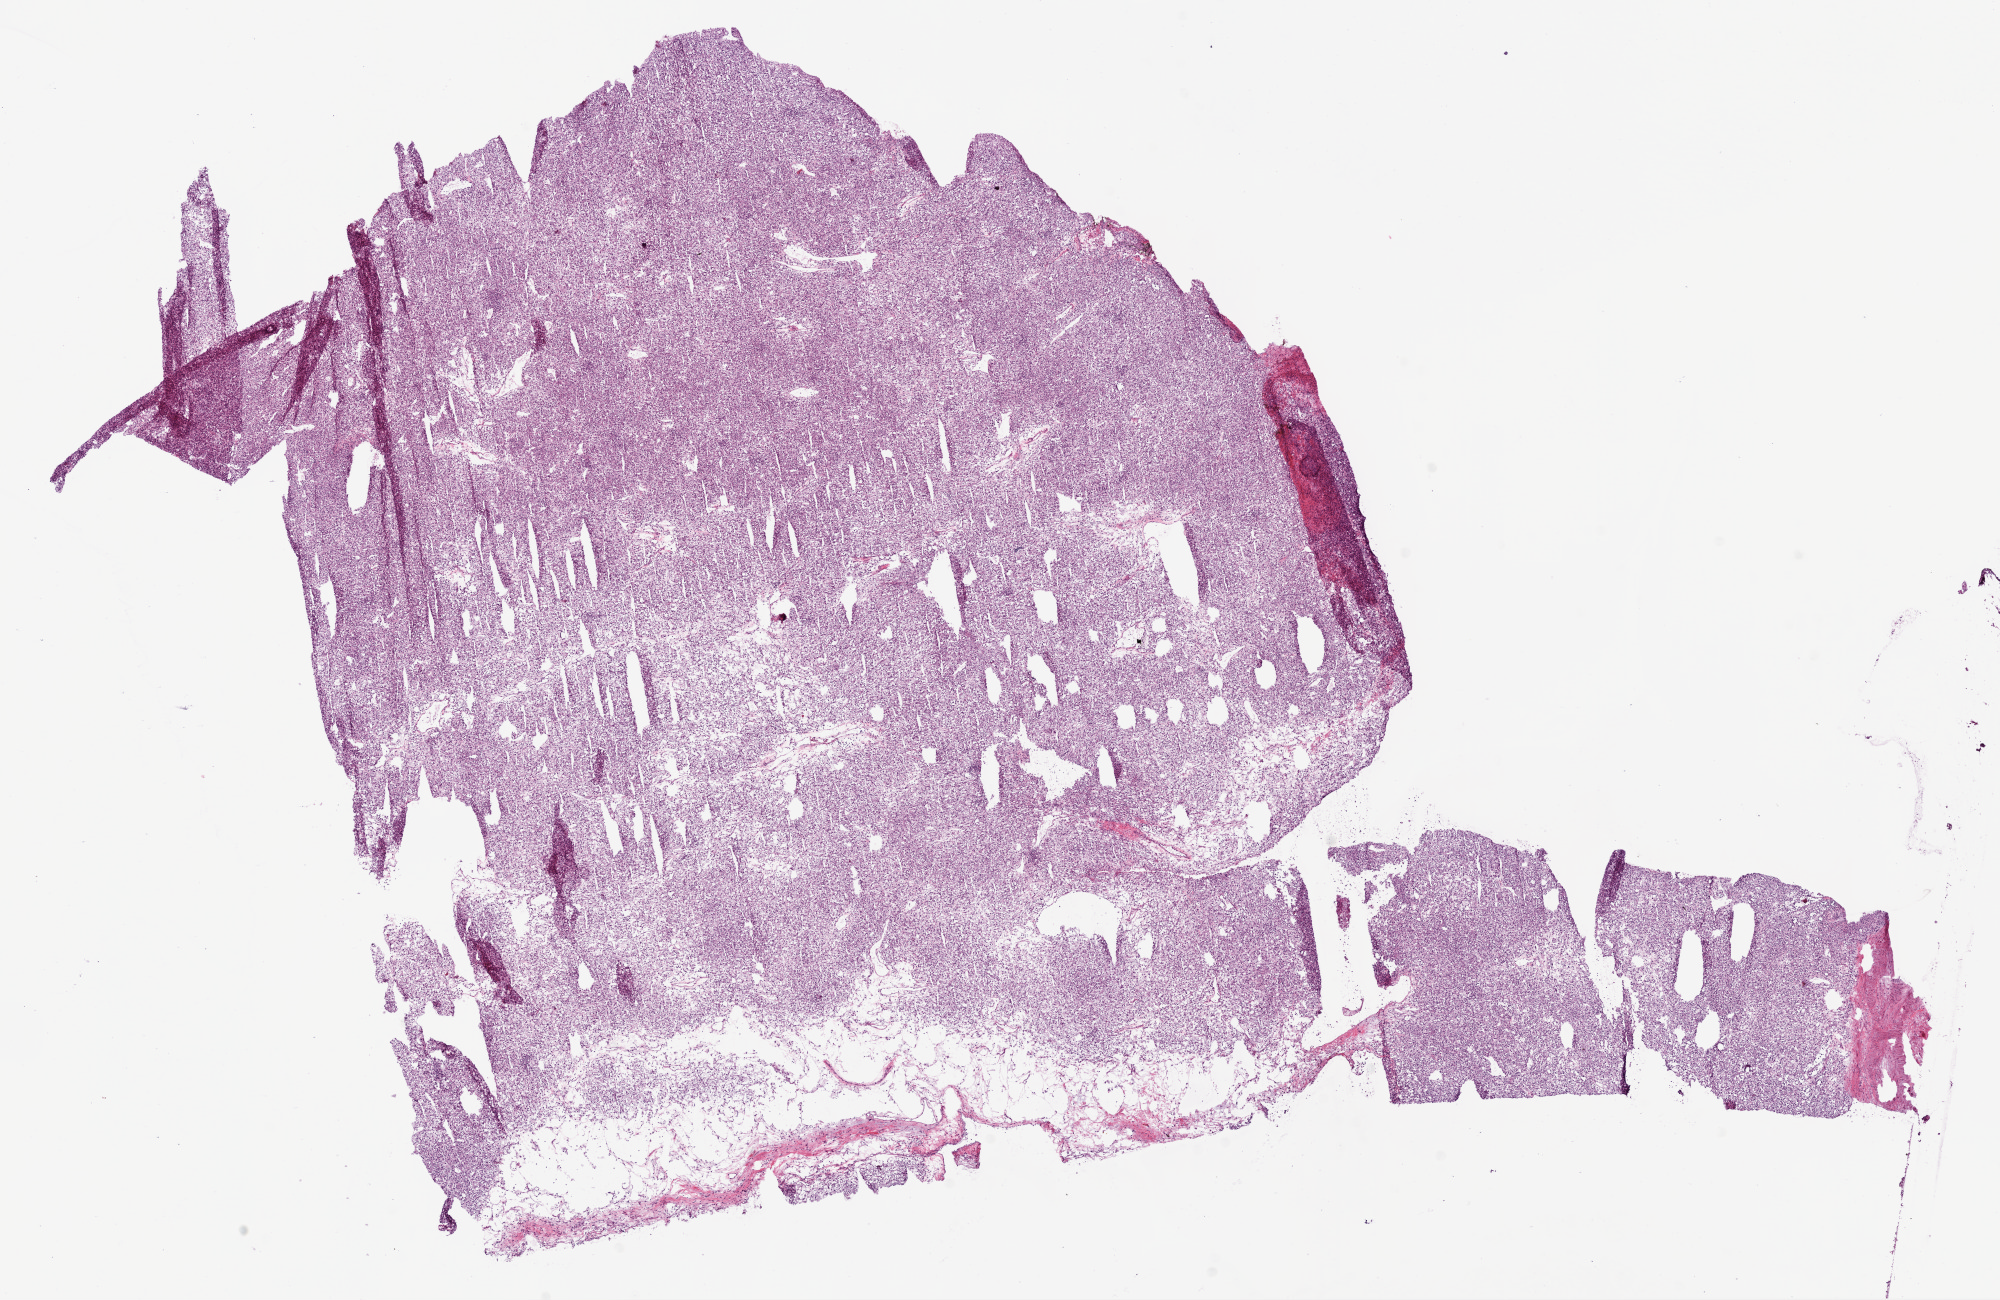
Digitized Hematoxylin and eosin (H&E) stained tissue section (whole slide), a low-resolution overview of the entire scanned area, about 16.0 x 10.4 mm; frozen section; kidney, primary tumour sample. Male, age 61 years at initial diagnosis. Slide review estimates, as recorded: tumour cells 95%, tumour nuclei 98%.
Histologic diagnosis: Clear cell adenocarcinoma, NOS.